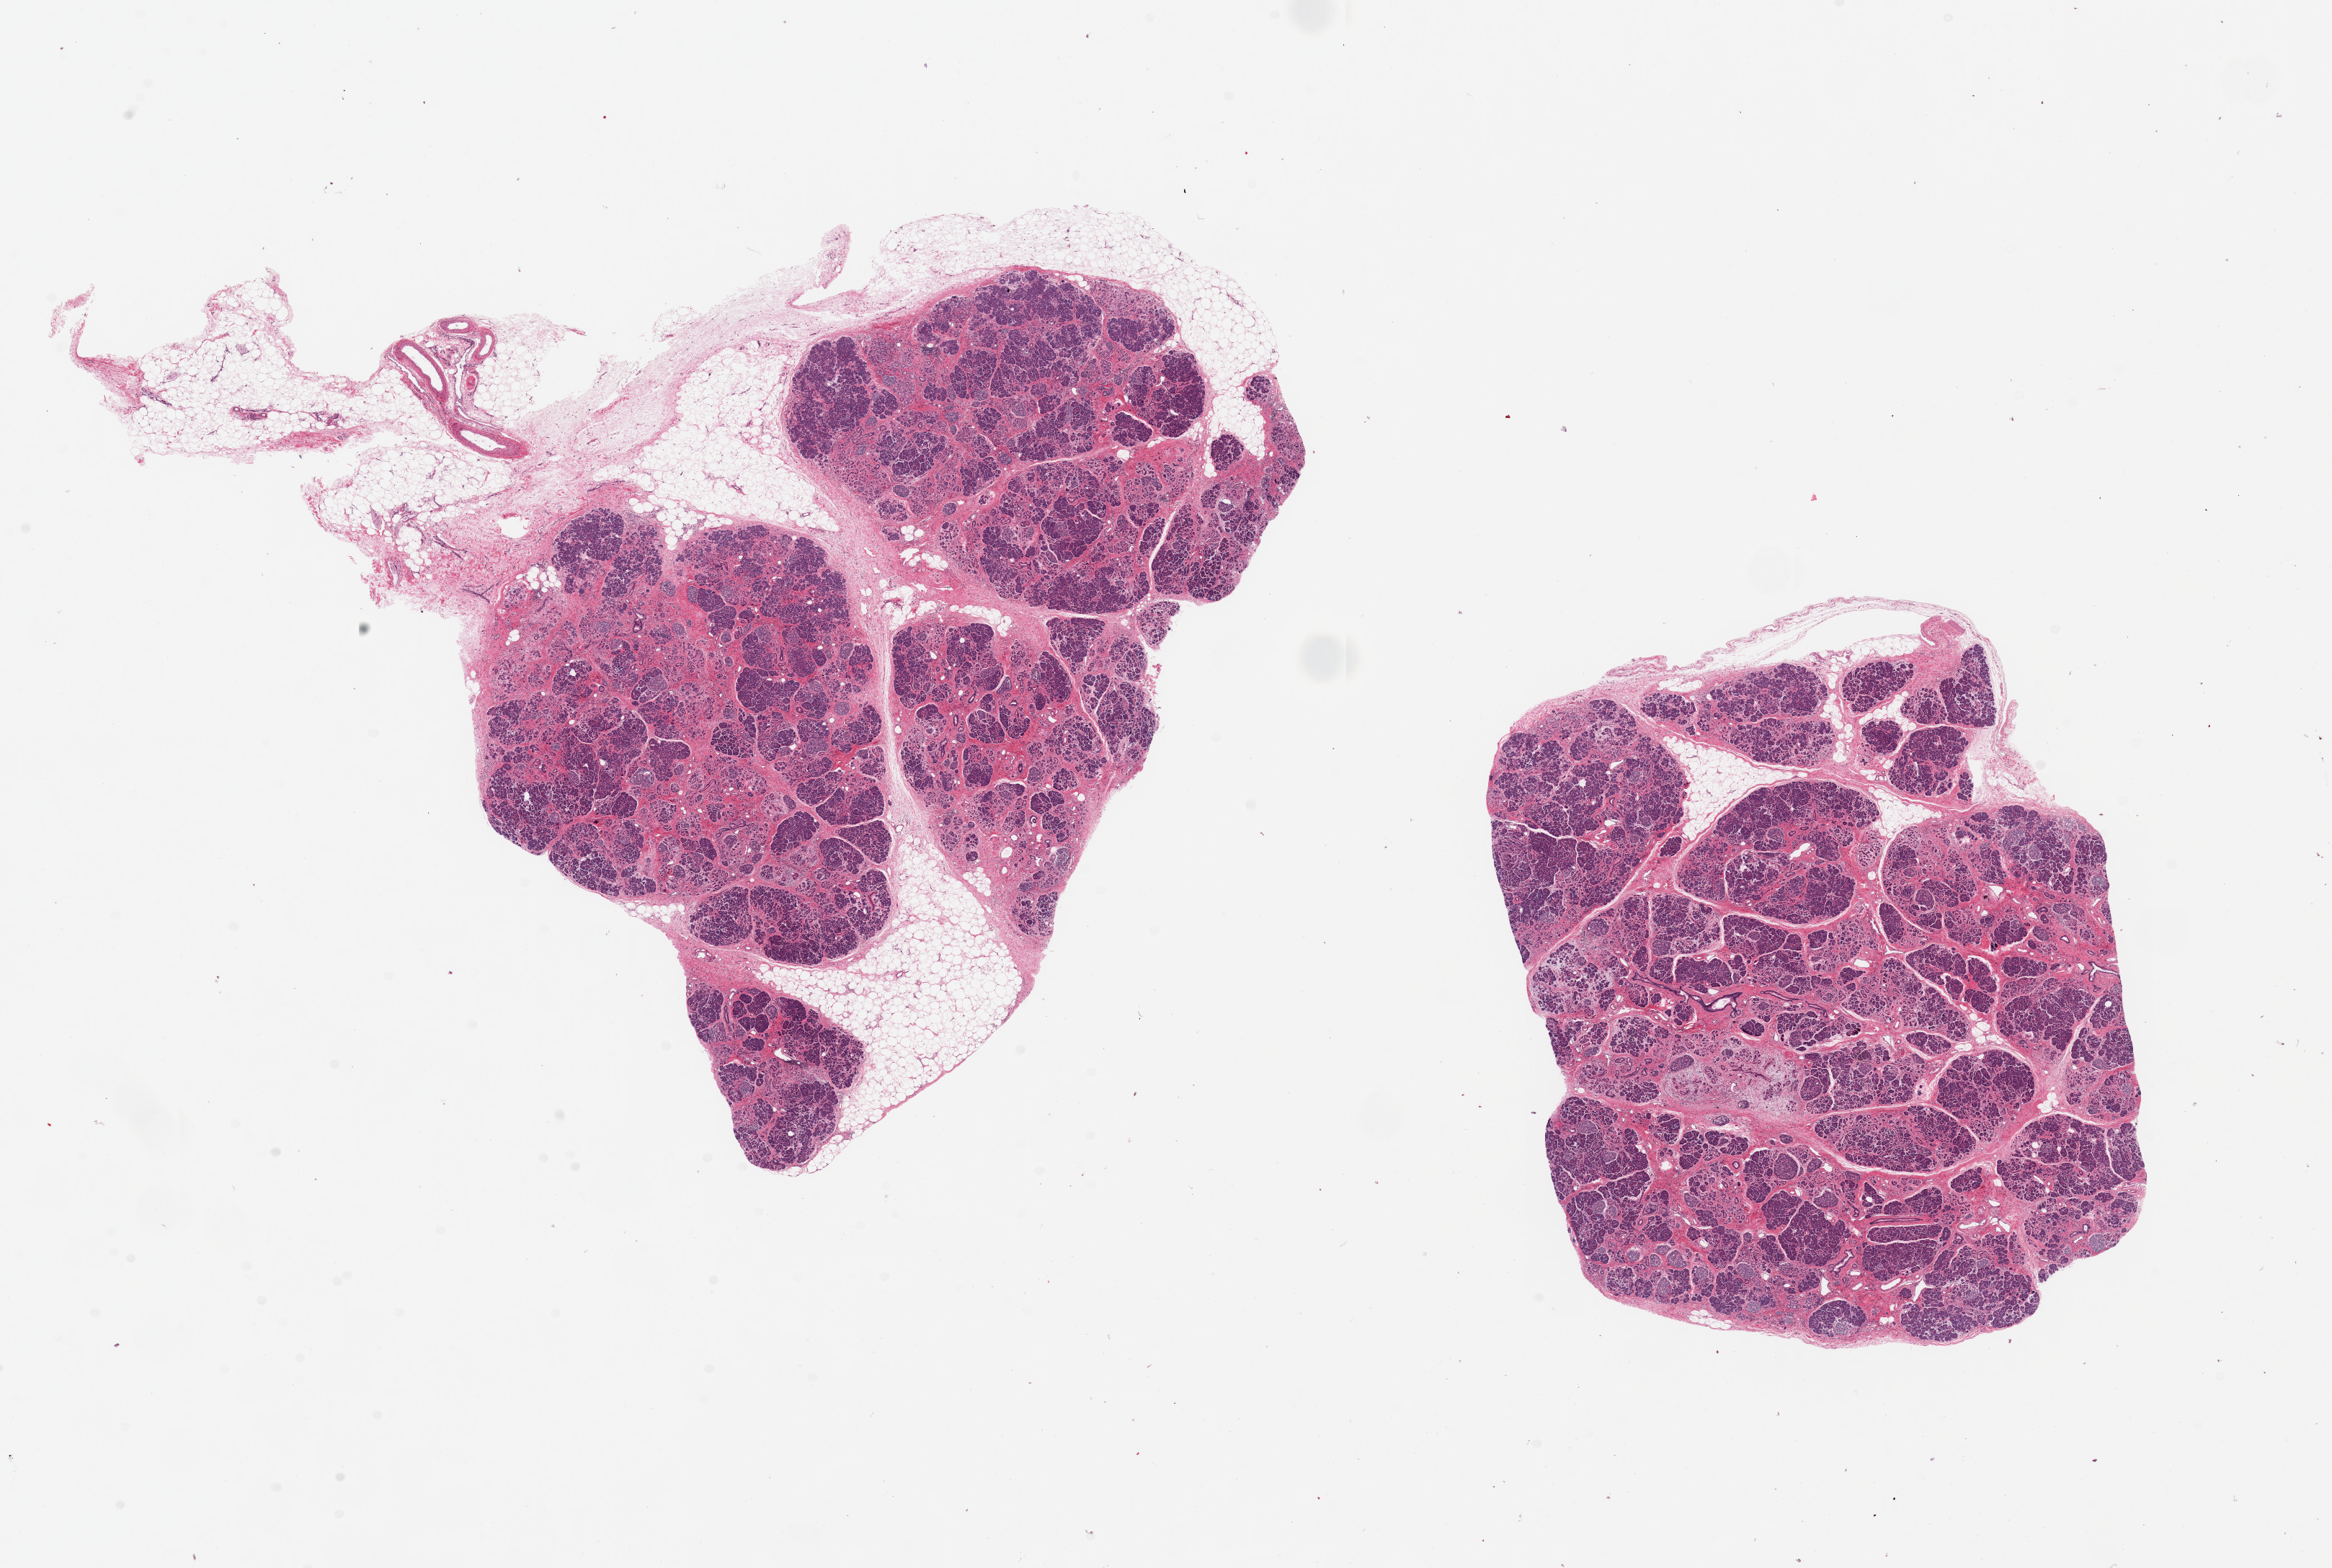
Digitized haematoxylin and eosin-stained section, low-resolution overview of the scanned area, about 25.6 x 17.2 mm, PAXgene-fixed, paraffin-embedded tissue, target tissue: pancreas, donor tissue sample. Donor sex: female.
Reviewer comment on this tissue sample: 2 pieces, 14x11 & 8x6mm; wlle preserved with areas of fibrosis; Islets well seen/preserved.